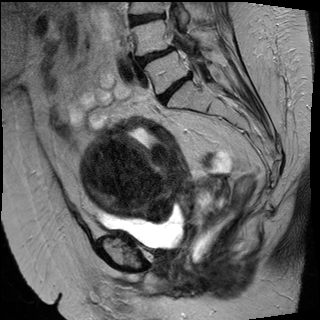
Pelvic MRI for cervical cancer, one sagittal slice. Slice 27 of 50 in the series (ordered by position). T2-weighted. 1.5 T. TE 89 ms, TR 4880 ms. 4 mm slice thickness. 320 × 320 image matrix. Patient: female, 50 years.
Outlined on this slice (manually delineated by an expert):
- uterus and cervix: bounding box (x1, y1, x2, y2) in pixels: (82, 115, 229, 224)